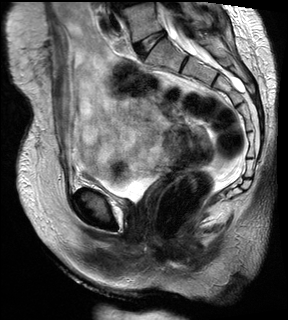
Pelvic MRI for cervical cancer, one sagittal slice; position 15 of 28 along the scan axis; T2-weighted; 1.5 T; TE 89 ms, TR 2740 ms; 4 mm slice thickness; 288 × 320 image matrix, field of view 234 × 260 mm. Patient: female, 59 years.
Structures marked on this image (outlined manually by an expert reader):
- uterus and cervix: bounding box [x1, y1, x2, y2] px = [162, 122, 213, 170]